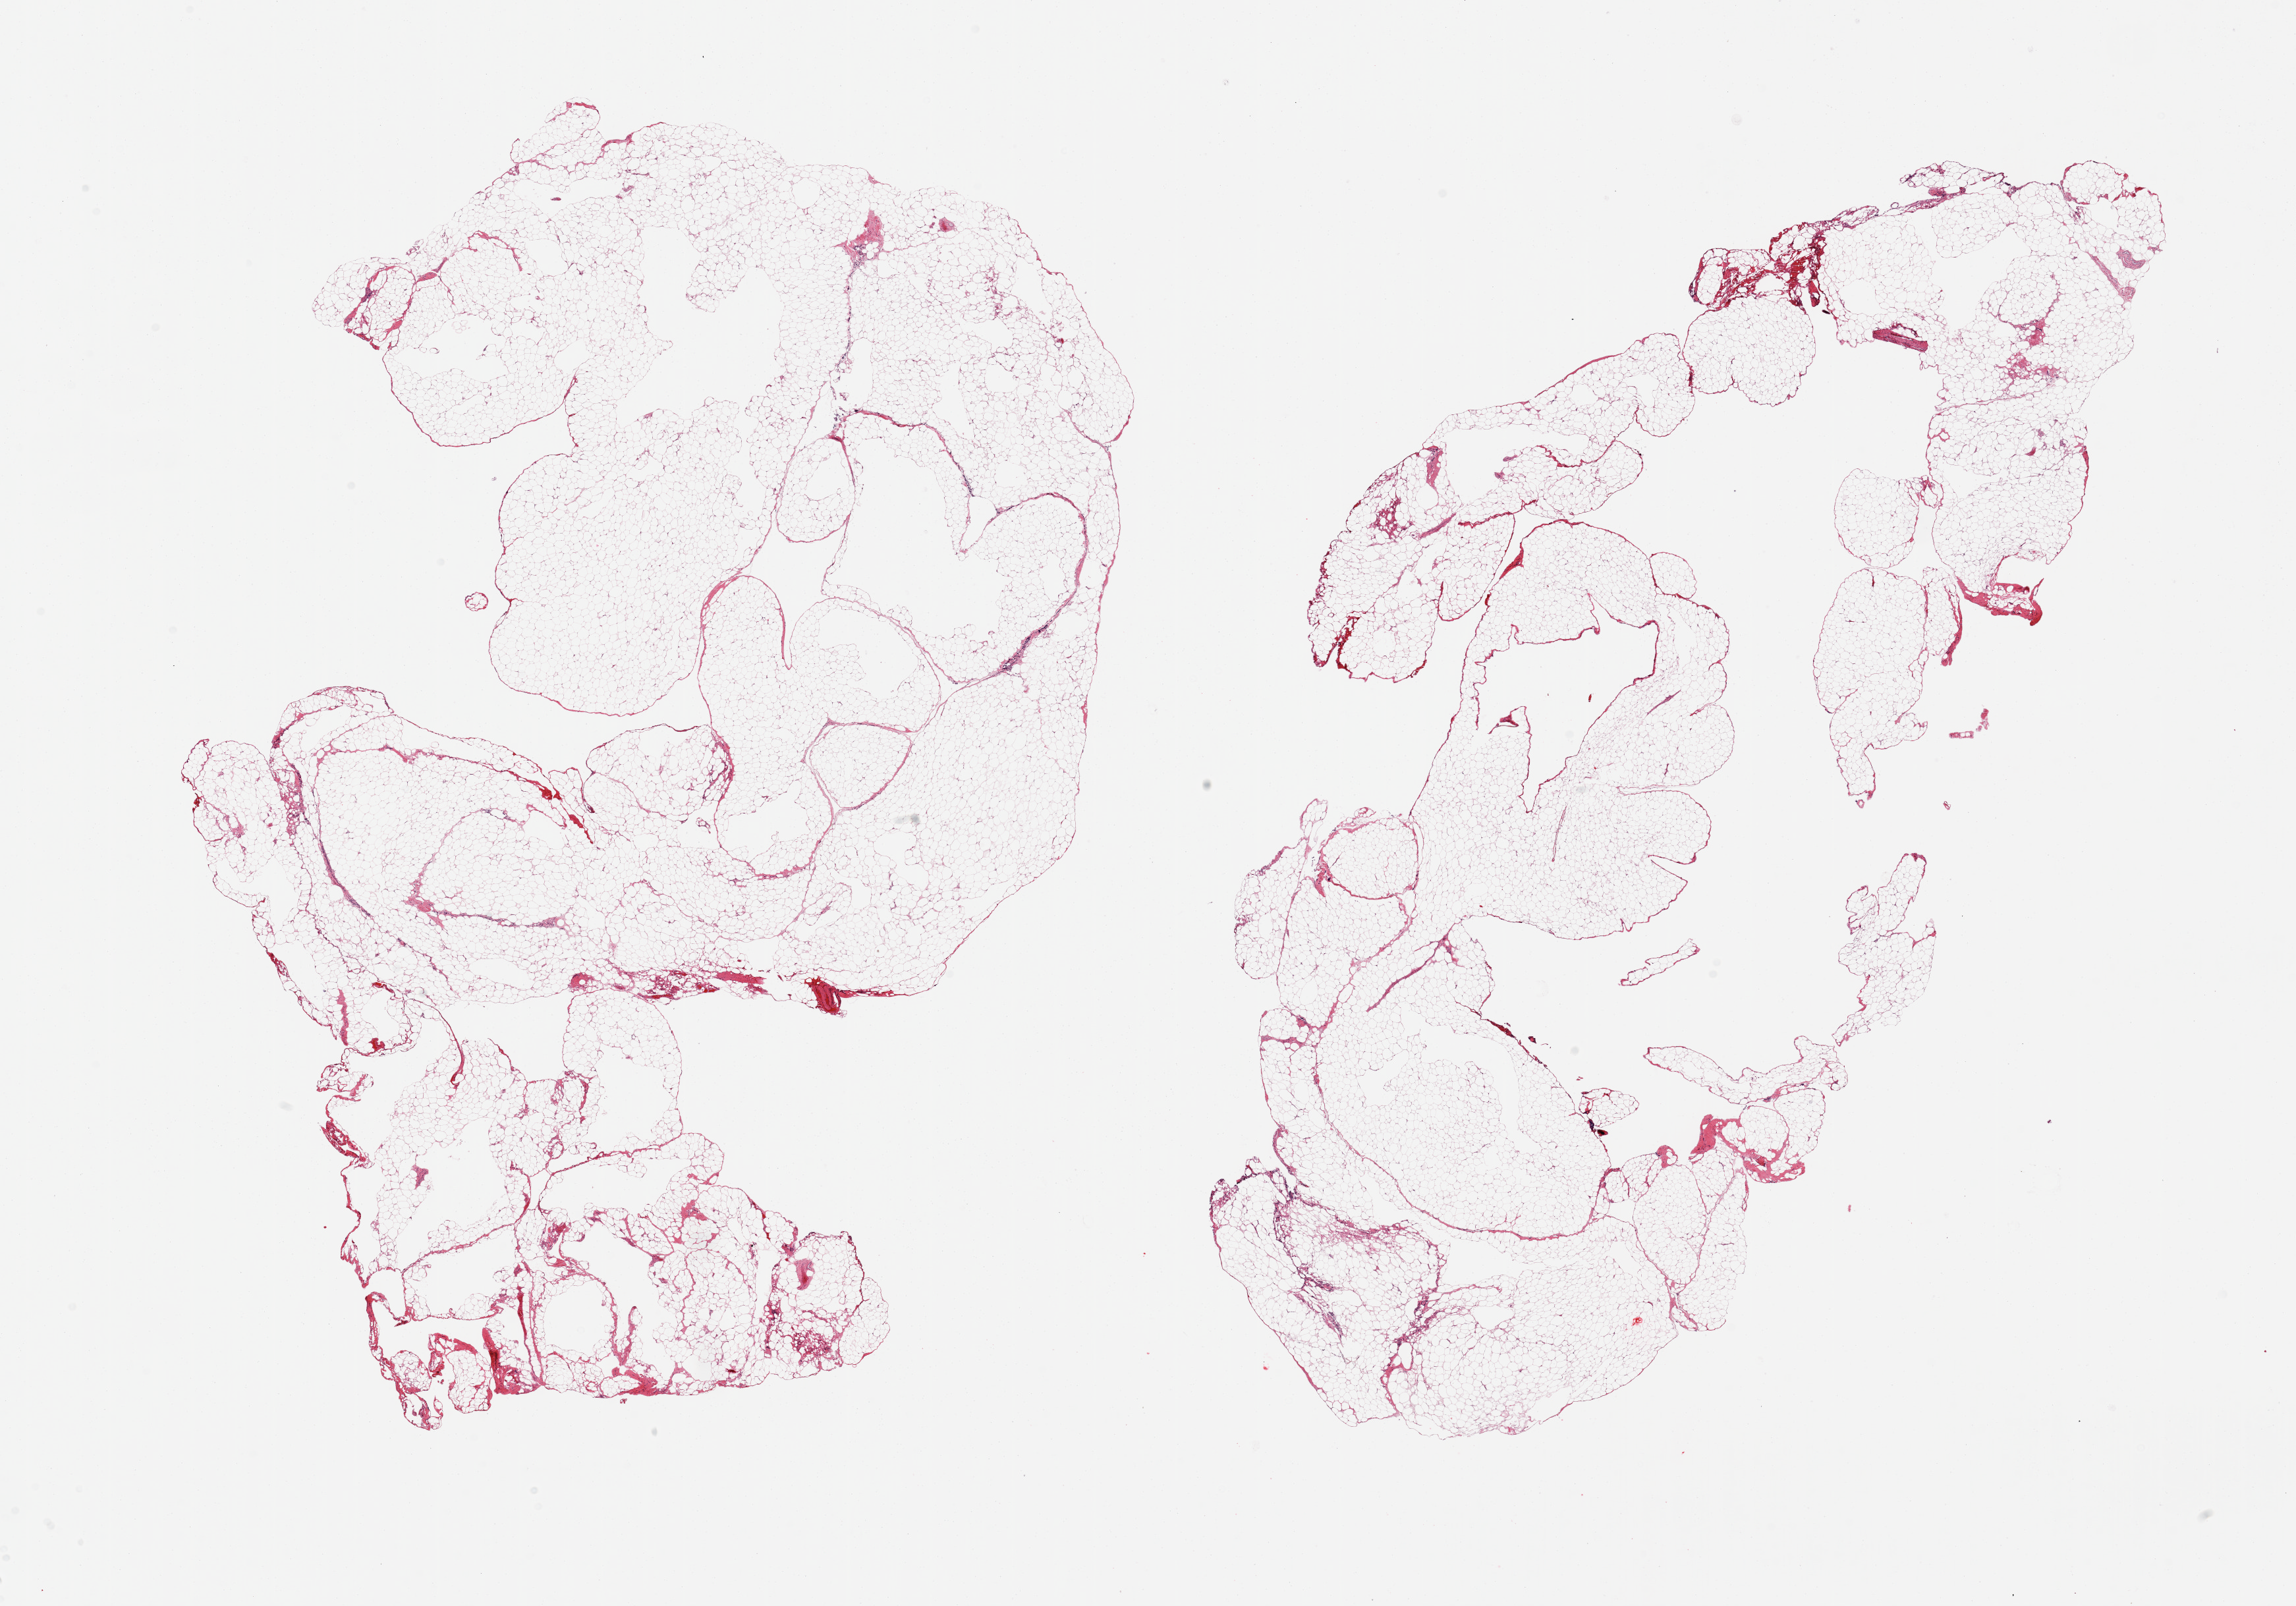
Hematoxylin and eosin (H&E) whole-slide image, brightfield, low-resolution overview of the scanned area, about 27.6 x 19.3 mm (acquisition: 20x scan); PAXgene-fixed paraffin-embedded (PFPE) section; sampled site (target tissue): omentum; tissue donor sample. Donor: male.
Pathologist's review note for this sample: 2 pieces, minimal fat/fascia.